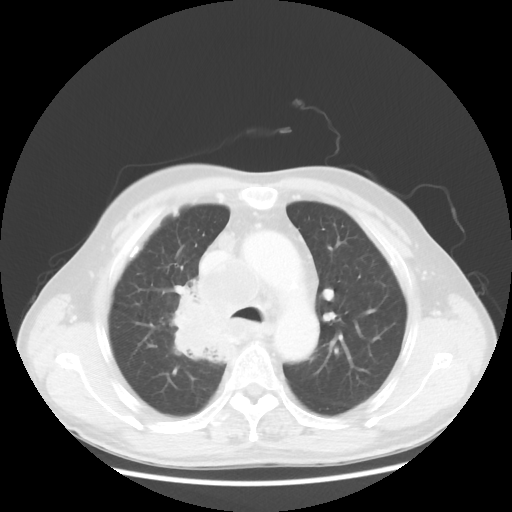
Chest CT, one axial slice; reconstruction kernel STANDARD; 100 kVp; lung window (W 1500 / L -600 HU); 5 mm slice thickness; 512 × 512 image matrix, field of view 382 × 382 mm. Male patient, age 64 years. Case-level facts recorded for this patient, not image findings: clinical TNM (as recorded): T3 N3 M0.
Outlined on this slice (bounding box drawn by a radiologist):
- lung tumour (recorded histology: small cell carcinoma): bounding box [x1, y1, x2, y2] px = [163, 283, 245, 375]